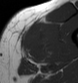
MRI of an extremity soft-tissue mass, one axial slice; slice 27 of 43 in the series (ordered by position); MR volume resampled by the dataset authors to the PET/CT grid (not the native acquisition matrix); 3.27 mm slice thickness; 78 × 83 image matrix. Male patient. Case-level facts recorded for this patient, not image findings: histological type: pleiomorphic leiomyosarcoma; grade: high; site of the primary tumour: left thigh.
Annotated regions visible in this slice (expert contour drawn on MRI and transferred to this co-registered scan by the dataset authors):
- gross tumour volume including surrounding oedema: bounding box (x1, y1, x2, y2) in pixels: (20, 22, 53, 61)
- gross tumour volume (mass): (22, 28, 46, 59)